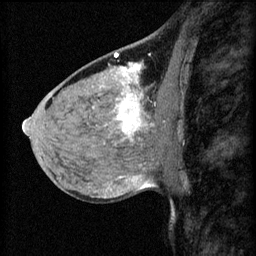
Breast MRI (dynamic contrast-enhanced), one sagittal slice; slice 36 of 60 in the series (ordered by position); 3 images stored at this slice position (order not interpretable as contrast timing); 1.5 T; TE 4.2 ms, TR 8.2 ms; 2.2 mm slice thickness; 256 × 256 image matrix, field of view 180 × 180 mm. Female patient, age 40 years.
Structures marked on this image (semi-automatically segmented with operator editing):
- analysis volume of interest (the breast-tissue region the enhancement analysis was run in; not a lesion): bounding box [x1, y1, x2, y2] px = [108, 82, 175, 139]
- tumour enhancement mask (voxels above the 70 % enhancement threshold inside the analysis volume of interest): [116, 82, 155, 135]